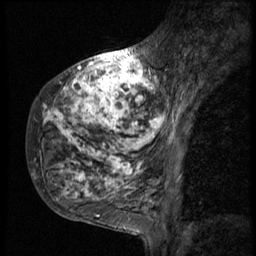
Breast MRI (dynamic contrast-enhanced), one sagittal slice; slice 17 of 58 in the series (ordered by position); 3 images stored at this slice position (order not interpretable as contrast timing); 1.5 T; TE 4.2 ms, TR 9 ms; 2.5 mm slice thickness; 256 × 256 image matrix. Female patient, age 50 years. From the clinical record (not read from this slice): setting: breast cancer imaged before/during neoadjuvant chemotherapy; receptor status: triple-negative.
Outlined on this slice (semi-automatically segmented with operator editing):
- analysis volume of interest (the breast-tissue region the enhancement analysis was run in; not a lesion): box from (x=27, y=48) to (x=186, y=214) px
- tumour enhancement mask (voxels above the 140 % enhancement threshold inside the analysis volume of interest): (x=34, y=48)–(x=186, y=201)